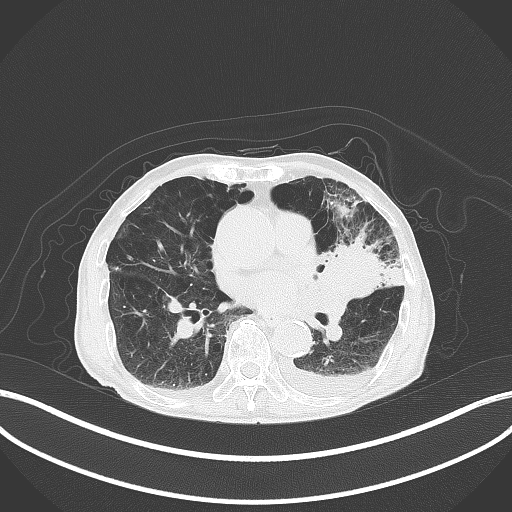
Chest CT, one axial slice; slice 184 of 227 in the series (ordered by position); reconstruction kernel B70f; 120 kVp; lung window (W 1500 / L -600 HU); 3 mm slice thickness; 512 × 512 image matrix. Male patient, age 90 years or older. Case-level facts recorded for this patient, not image findings: clinical TNM (as recorded): T2b N1 M0.
Annotated regions visible in this slice (bounding box drawn by a radiologist):
- lung tumour (recorded histology: squamous cell carcinoma): box from (x=318, y=234) to (x=404, y=306) px